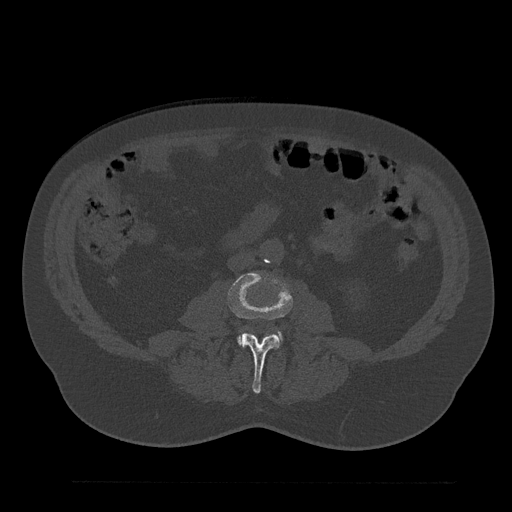
CT including the spine, one axial slice. Position 13 of 797 along the scan axis. Reconstruction kernel Br40s/3. 120 kVp. Bone window (W 1800 / L 400 HU). 512 × 512 image matrix, field of view 430 × 430 mm. Male patient, age 61 years. From the clinical record (not read from this slice): primary cancer: prostate.
Annotated regions visible in this slice (semi-automatically segmented with operator editing):
- L3 vertebra: bounding box [x1, y1, x2, y2] px = [228, 272, 292, 394]
- L4 vertebra: [238, 335, 242, 344]